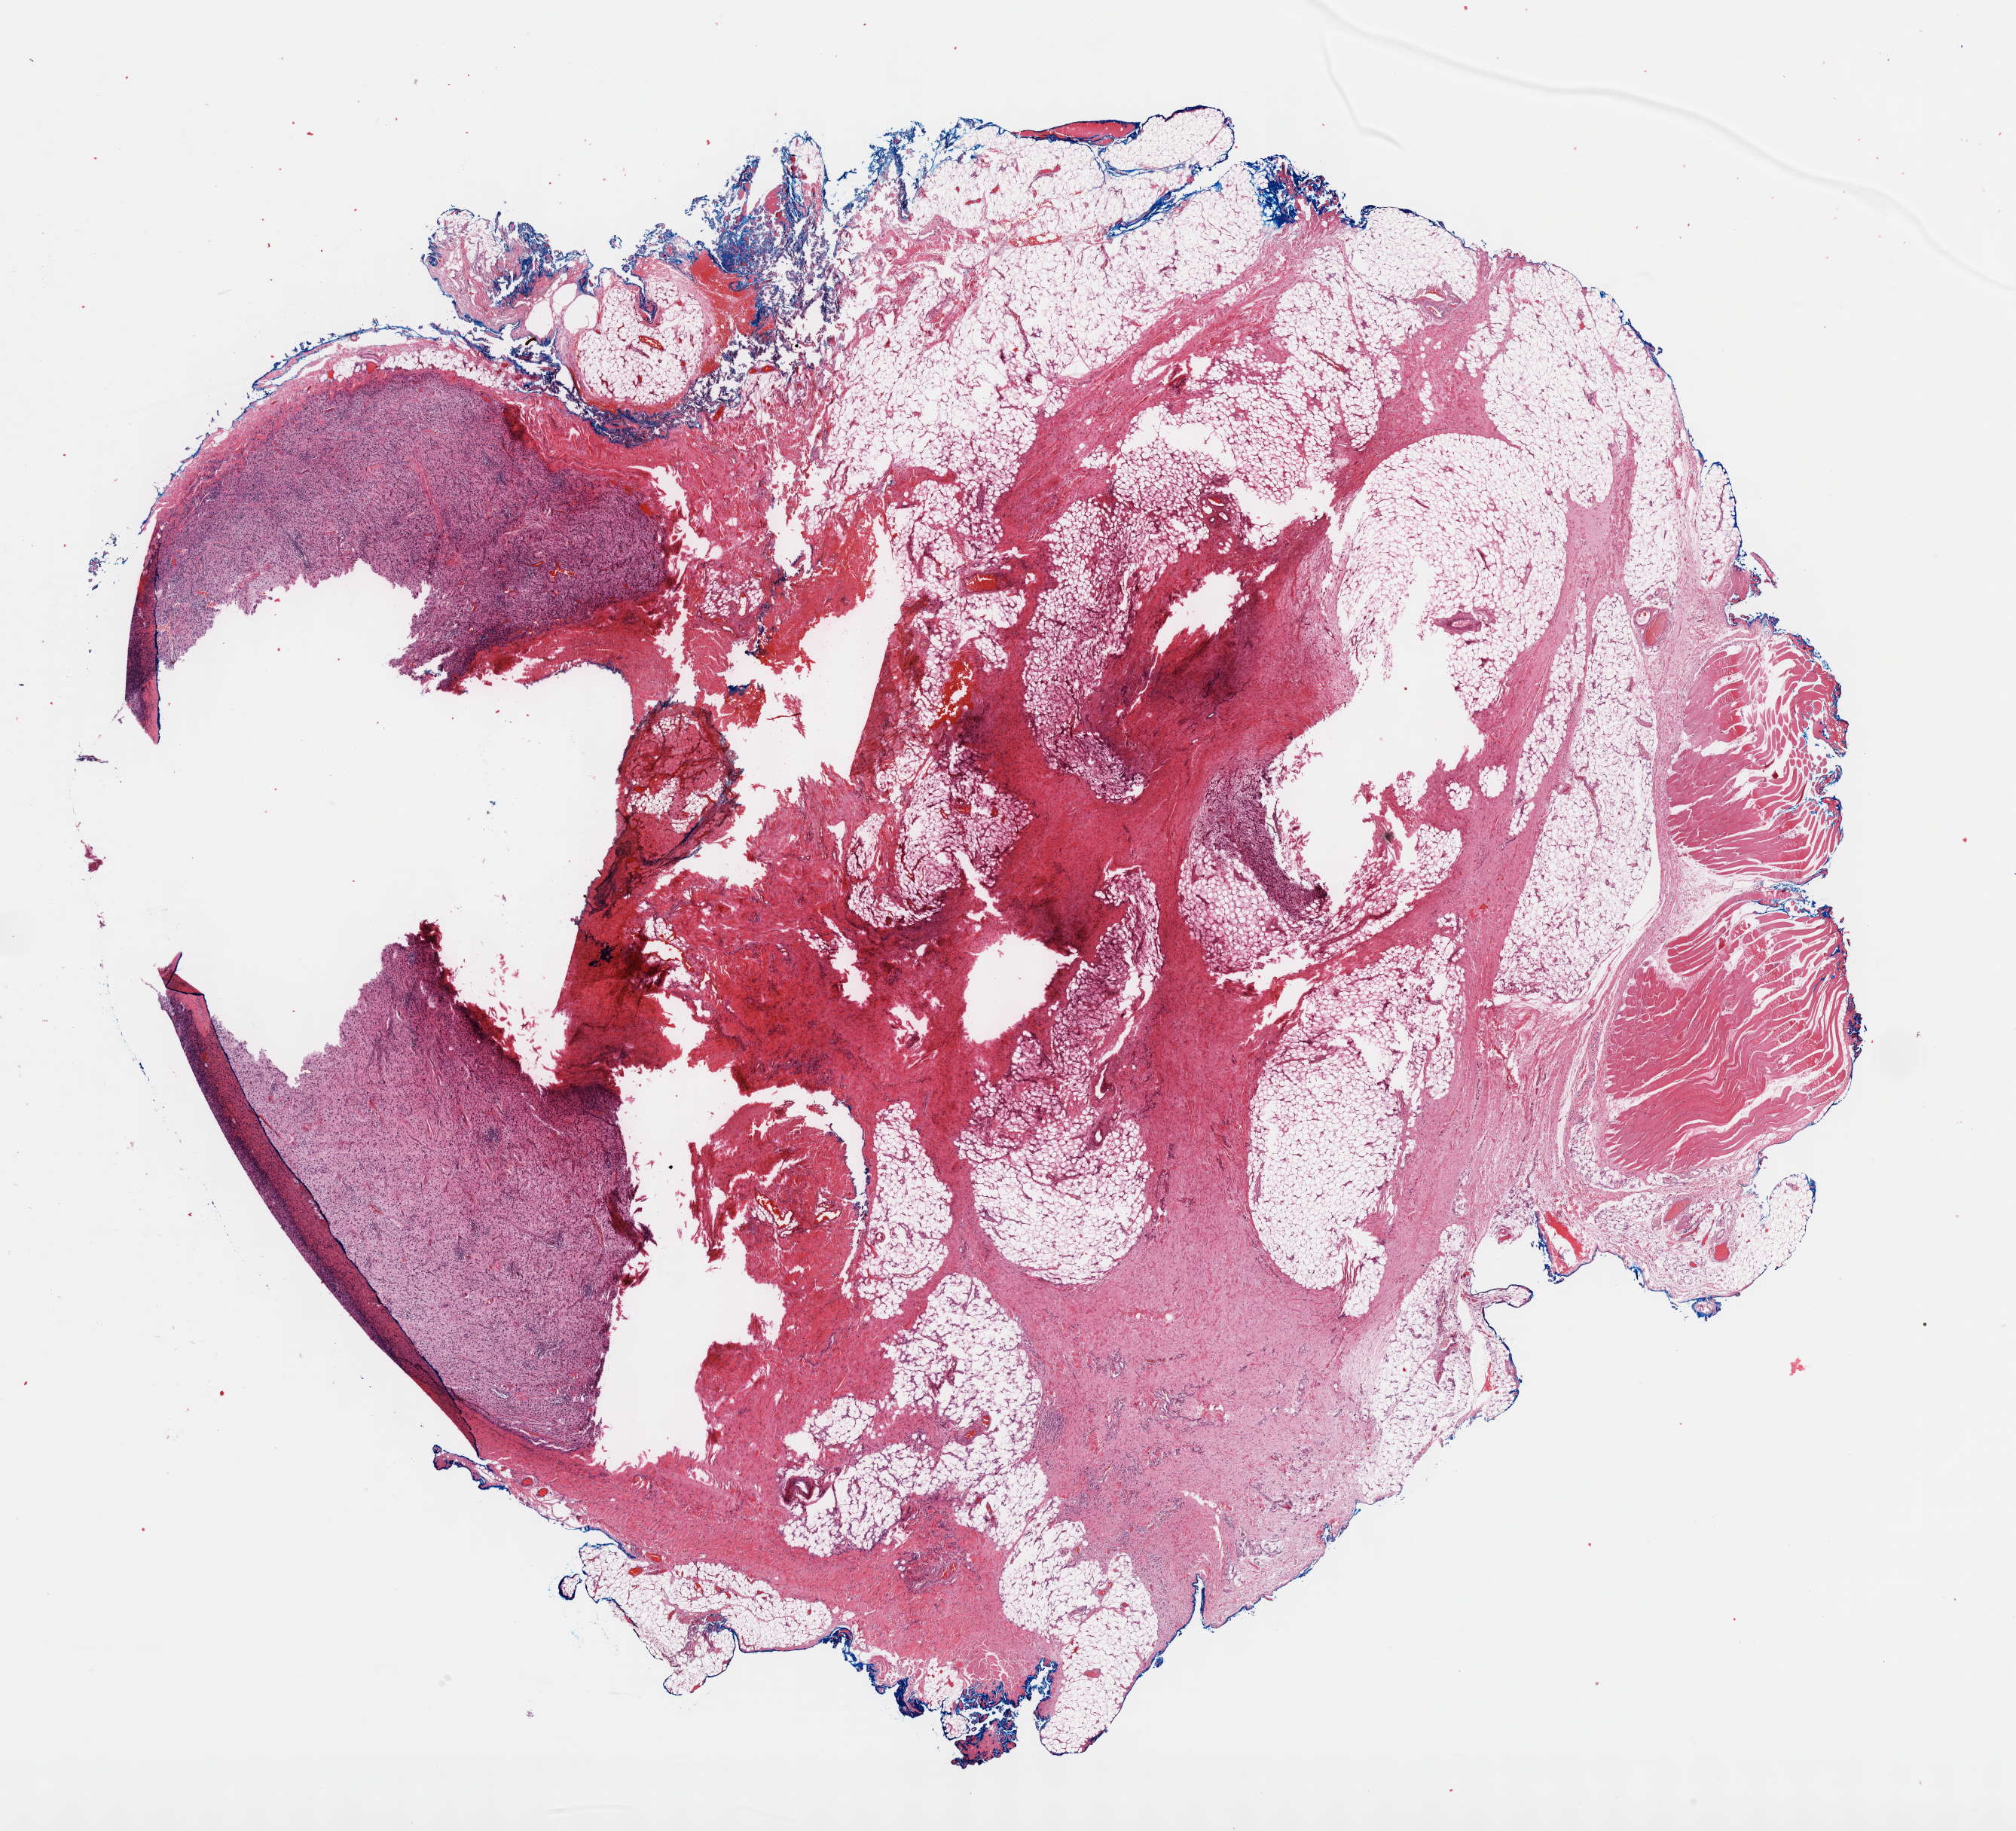
Digitized H&E-stained tissue section (whole slide), low-resolution overview of the scanned area, about 21.6 x 19.7 mm. Formalin-fixed paraffin-embedded (FFPE) diagnostic section. Connective, subcutaneous and other soft tissues, primary tumour sample. Male, age 35 years at initial diagnosis.
Histologic diagnosis: Fibromyxosarcoma (connective, subcutaneous and other soft tissues of lower limb and hip).